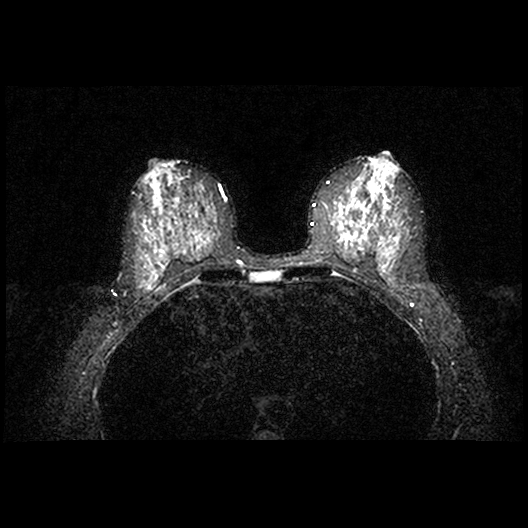
MRI of the breasts; 2 images, each one mid-volume slice chosen by position.
Image 1: axial T2-weighted / STIR image, slice 43 of 84.
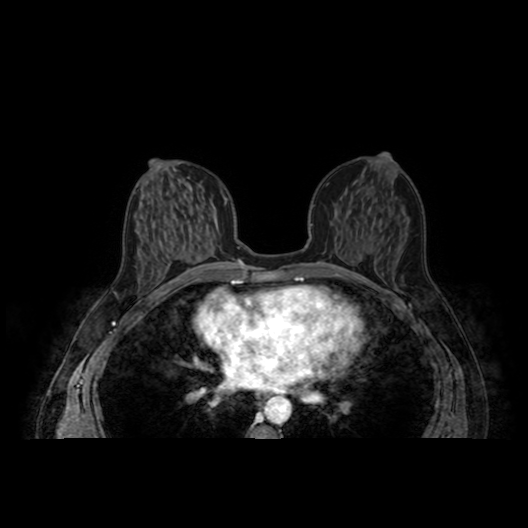
Image 2: axial dynamic contrast-enhanced T1-weighted image, series "AX BLISS_AUTO SENSE", slice 43 of 84, dynamic phase 6 of 10, 4 mm slice thickness.
Patient-level pathology facts (from the clinical record, not from the images): pathology diagnosis: infiltrating ductal CA (right breast); receptor status (as recorded): ER pos (strongly), PR pos (weak), HER2 moderate by fish; Ki-67 (as recorded): high prolif; pathology report notes: RIGHT BREAST MASS: INFILTRATING DUCTAL CARCINOMA, MODIFIED SCARFF-BLOOM-RICHARDSON GRADE-II/III. A 5% INTRADUCTAL CARCINOMA COMPONENT, COMEDO TYPE, NUCLEAR GRADE III/III, IS ALSO PRESENT.re-bx [date] was no residual tumor.